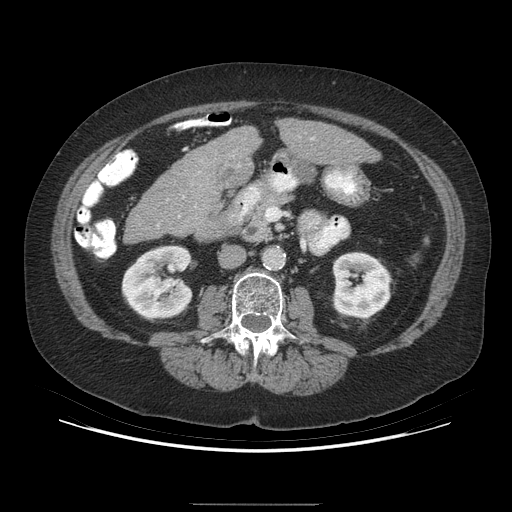
Contrast-enhanced abdominal CT (liver protocol), one axial slice; position 134 of 192 along the scan axis; reconstruction kernel STANDARD; 140 kVp; soft-tissue window (W 400 / L 40 HU); 2.5 mm slice thickness; 512 × 512 image matrix. Case-level facts recorded for this patient, not image findings: diagnosis: hepatocellular carcinoma (patient treated with transarterial chemoembolisation; whether this scan precedes or follows treatment is not stated here); TNM stage (as recorded): Stage-I; Child-Pugh class: A; tumour differentiation: moderately differentiated; tumour nodularity: uninodular.
Annotated regions visible in this slice (semi-automatically segmented with operator editing):
- liver parenchyma outside the tumour (the mass and vessels are separate outlines, so this box may not span the whole liver): bounding box <124,120,380,242> (left, top, right, bottom; pixels)
- mass: <215,151,254,191>